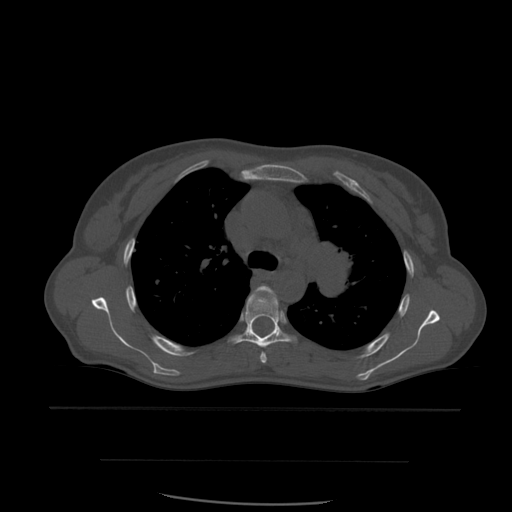
CT including the spine, one axial slice. Slice 413 of 574 in the series (ordered by position). Bone window (W 1800 / L 400 HU). 1.25 mm slice thickness. 512 × 512 image matrix, field of view 392 × 392 mm. Patient age 48 years. From the clinical record (not read from this slice): primary cancer: lung.
Outlined on this slice (semi-automatically segmented with operator editing):
- T4 vertebra: bounding box <253,286,275,363> (left, top, right, bottom; pixels)
- T5 vertebra: <231,290,297,348>